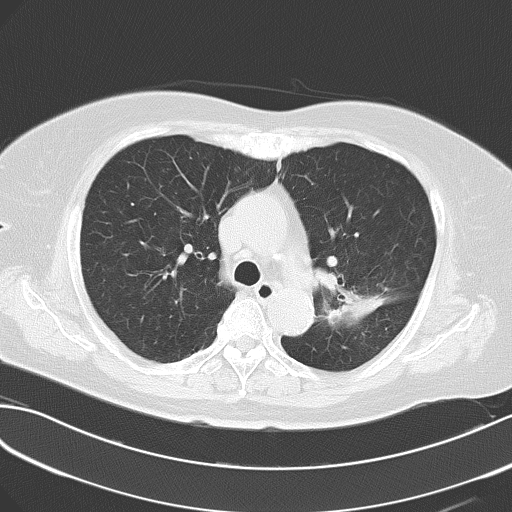
Chest CT, one axial slice; position 47 of 62 along the scan axis; reconstruction kernel B70f; 120 kVp; lung window (W 1500 / L -600 HU); 512 × 512 image matrix, field of view 353 × 353 mm. Patient: female, 70 years. Case-level facts recorded for this patient, not image findings: clinical TNM (as recorded): T2 N0 M0.
Outlined on this slice (rectangle marked by the reading radiologist):
- lung tumour (recorded histology: adenocarcinoma): bounding box <325,286,389,328> (left, top, right, bottom; pixels)